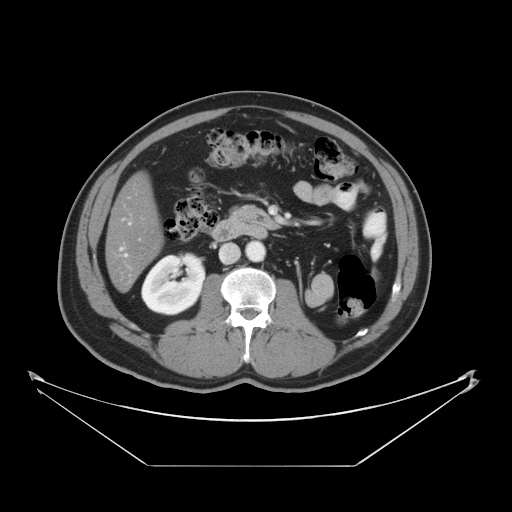
Contrast-enhanced abdominal CT, one axial slice; slice 15 of 46 in the series (ordered by position); reconstruction kernel STANDARD; 120 kVp; soft-tissue window (W 400 / L 40 HU); 5 mm slice thickness; 512 × 512 image matrix, field of view 465 × 465 mm. Male patient, age 57 years. Case-level facts recorded for this patient, not image findings: diagnosis: colorectal cancer liver metastases, imaged before liver resection; multiple liver metastases: no; largest metastasis: 3.3 cm; disease in both lobes: no.
Outlined on this slice (outlined manually by an expert reader):
- liver: bounding box [x1, y1, x2, y2] px = [106, 175, 162, 289]
- planned liver remnant (the part of the liver to remain after resection): [106, 175, 162, 289]
- portal vein (with intrahepatic branches): [125, 254, 127, 257]